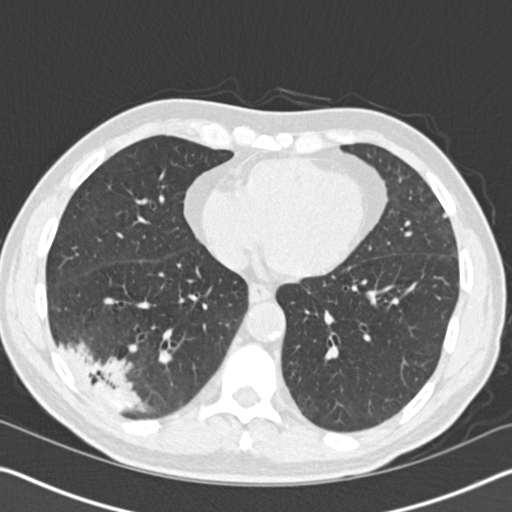
Axial slice from a low-dose chest CT screening exam, baseline screening round, lung window (W 1500 / L -600 HU), standard (soft-tissue) reconstruction kernel (B30f), 512 × 512 image matrix. Male participant, aged 61 years at enrolment. Current smoker at enrolment.
Lesion marked by an expert reader, bounding box (x1, y1, x2, y2) in pixels: (37, 312, 152, 421). Reader record for this screening exam (exam-level; its link to the box is not recorded): non-calcified nodule or mass ≥4 mm, right lower lobe, 52 × 36 mm, spiculated (stellate) margins, soft tissue attenuation. Participant outcome: lung cancer diagnosed 392 days after this screen (after the second annual screen) — bronchiolo-alveolar adenocarcinoma, NOS, right lower lobe, moderately differentiated (G2), stage IIIB (AJCC 6th edition), 90 mm at pathology.